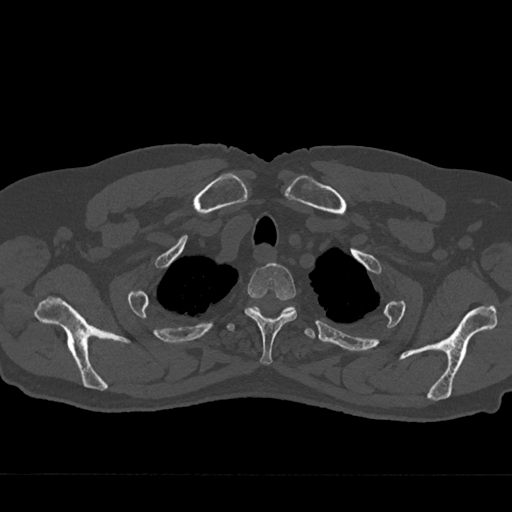
CT including the spine, one axial slice. Reconstruction kernel Br40s/3. 120 kVp. Bone window (W 1800 / L 400 HU). 0.5 mm slice thickness. 512 × 512 image matrix, field of view 377 × 377 mm. Male patient, age 75 years. Case-level facts recorded for this patient, not image findings: primary cancer: renal.
Outlined on this slice (semi-automatic segmentation, software-assisted and operator-edited):
- T2 vertebra: bounding box <244,263,297,365> (left, top, right, bottom; pixels)
- T3 vertebra: <227,306,316,339>